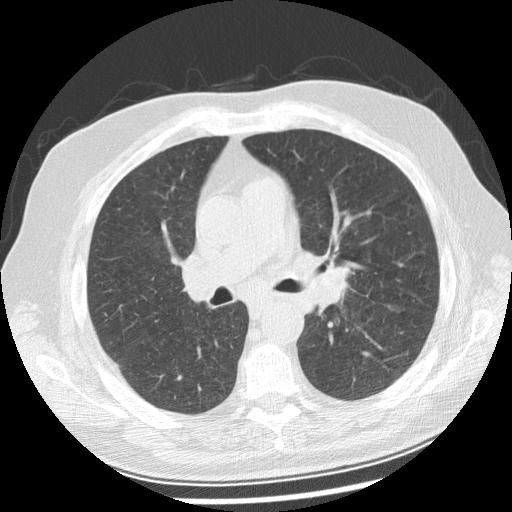
Axial slice from a low-dose chest CT screening exam, baseline screening round, lung window (W 1500 / L -600 HU), standard (soft-tissue) reconstruction kernel (STANDARD), 120 kVp. Male, age 70 years at enrolment. Current smoker at enrolment.
Lesion marked by an expert reader, bounding box [x1, y1, x2, y2] px = [282, 242, 364, 310]. No non-calcified nodule or mass ≥4 mm was recorded by the screening reader at this exam. Later outcome: lung cancer diagnosed 29 days after this screen — squamous cell carcinoma, keratinizing, NOS, left main stem bronchus, moderately differentiated (G2), stage IIIB (AJCC 6th edition), 40 mm at pathology.